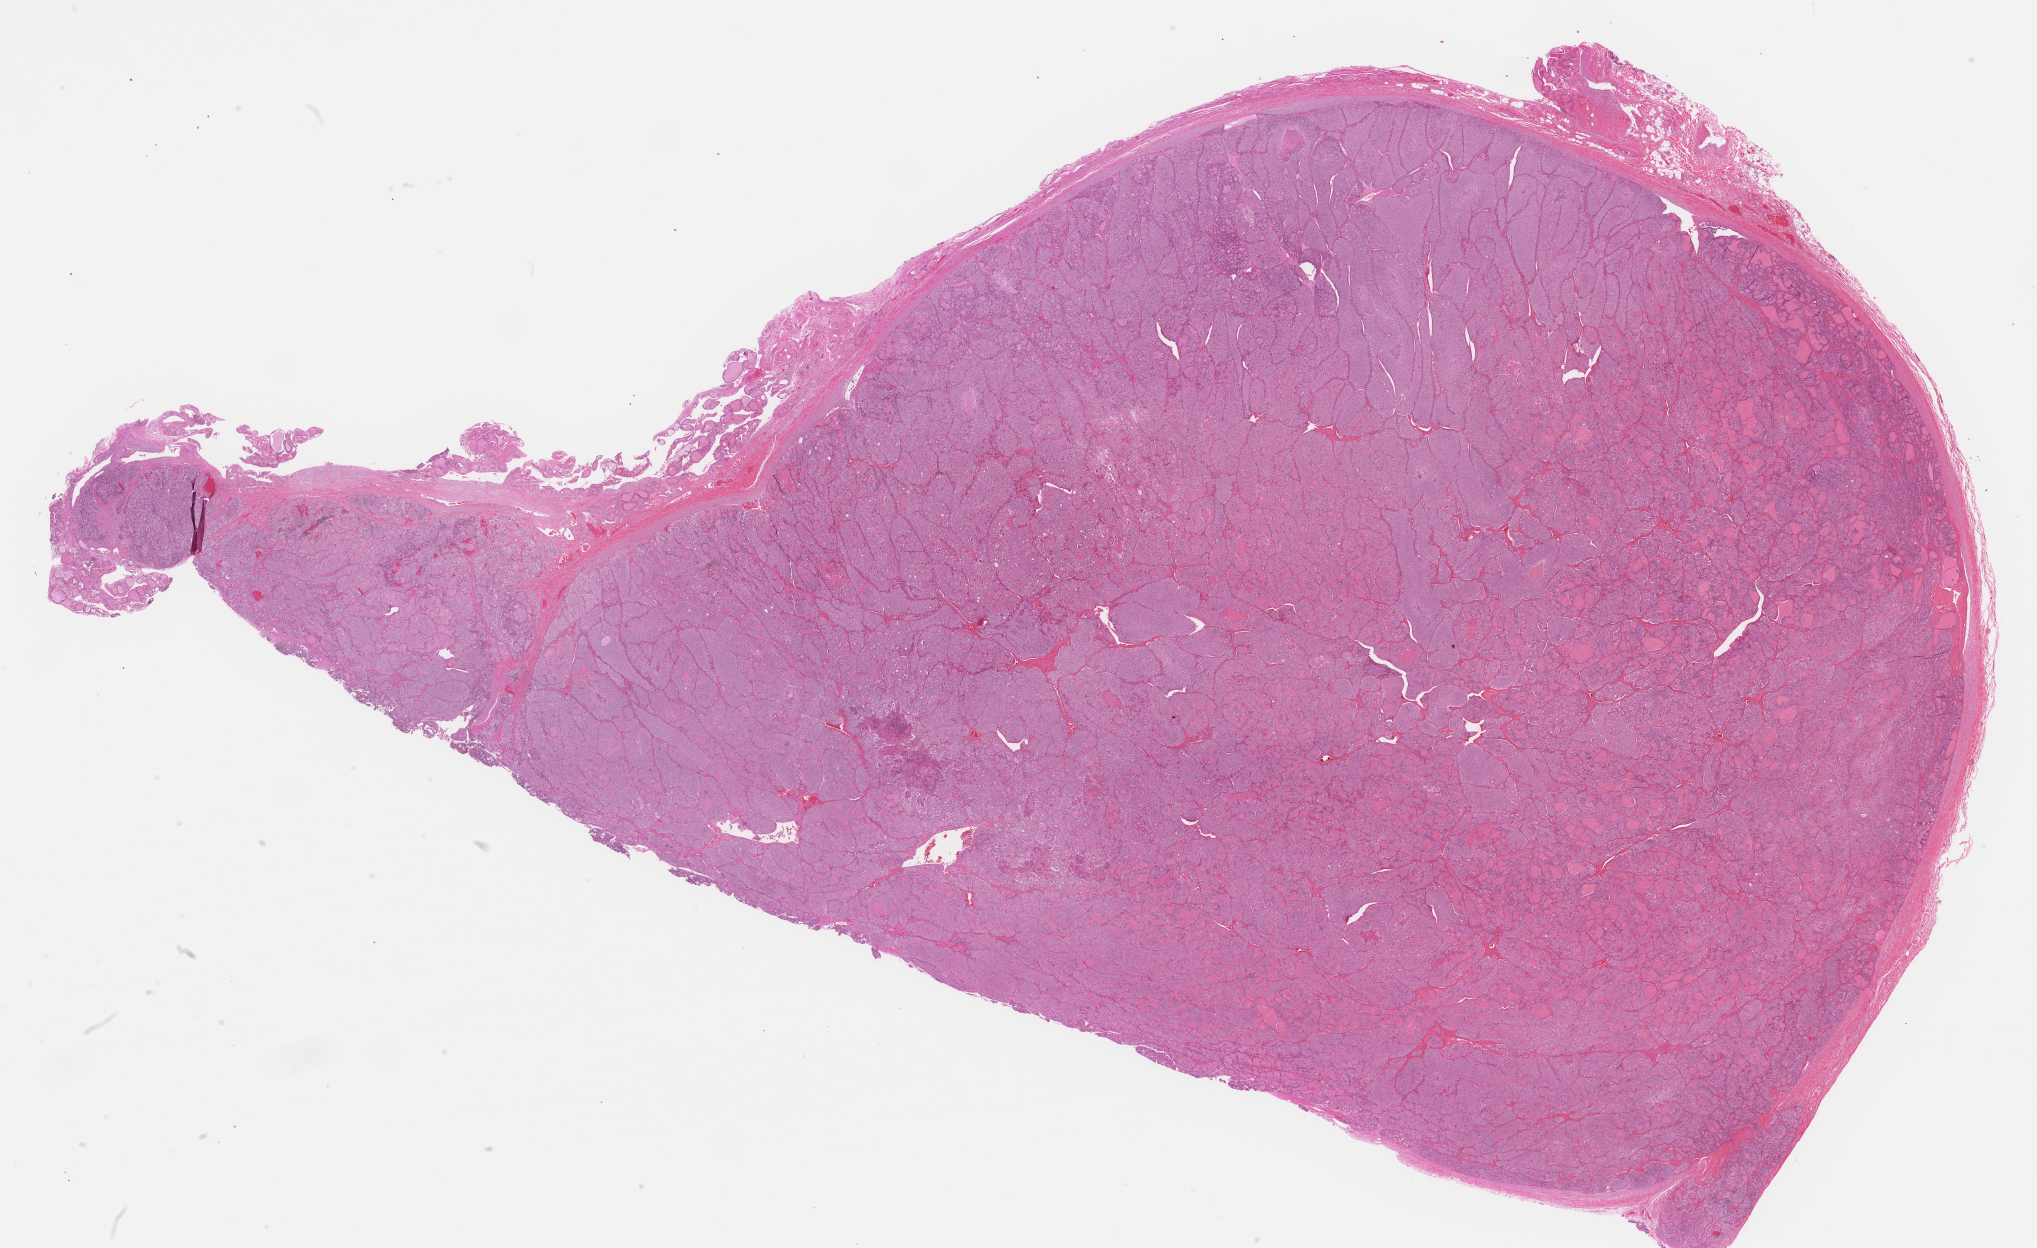
Digitized Hematoxylin and eosin (H&E) stained tissue section (whole slide) — low-resolution overview of the scanned area, about 32.1 x 19.7 mm (from a 40x scan); formalin-fixed paraffin-embedded (FFPE) diagnostic section; sample: primary tumour, thyroid. Male patient; age at initial diagnosis 75 years.
Diagnosis: Papillary adenocarcinoma, NOS (thyroid gland). AJCC pathologic stage: IV. Laterality: right.